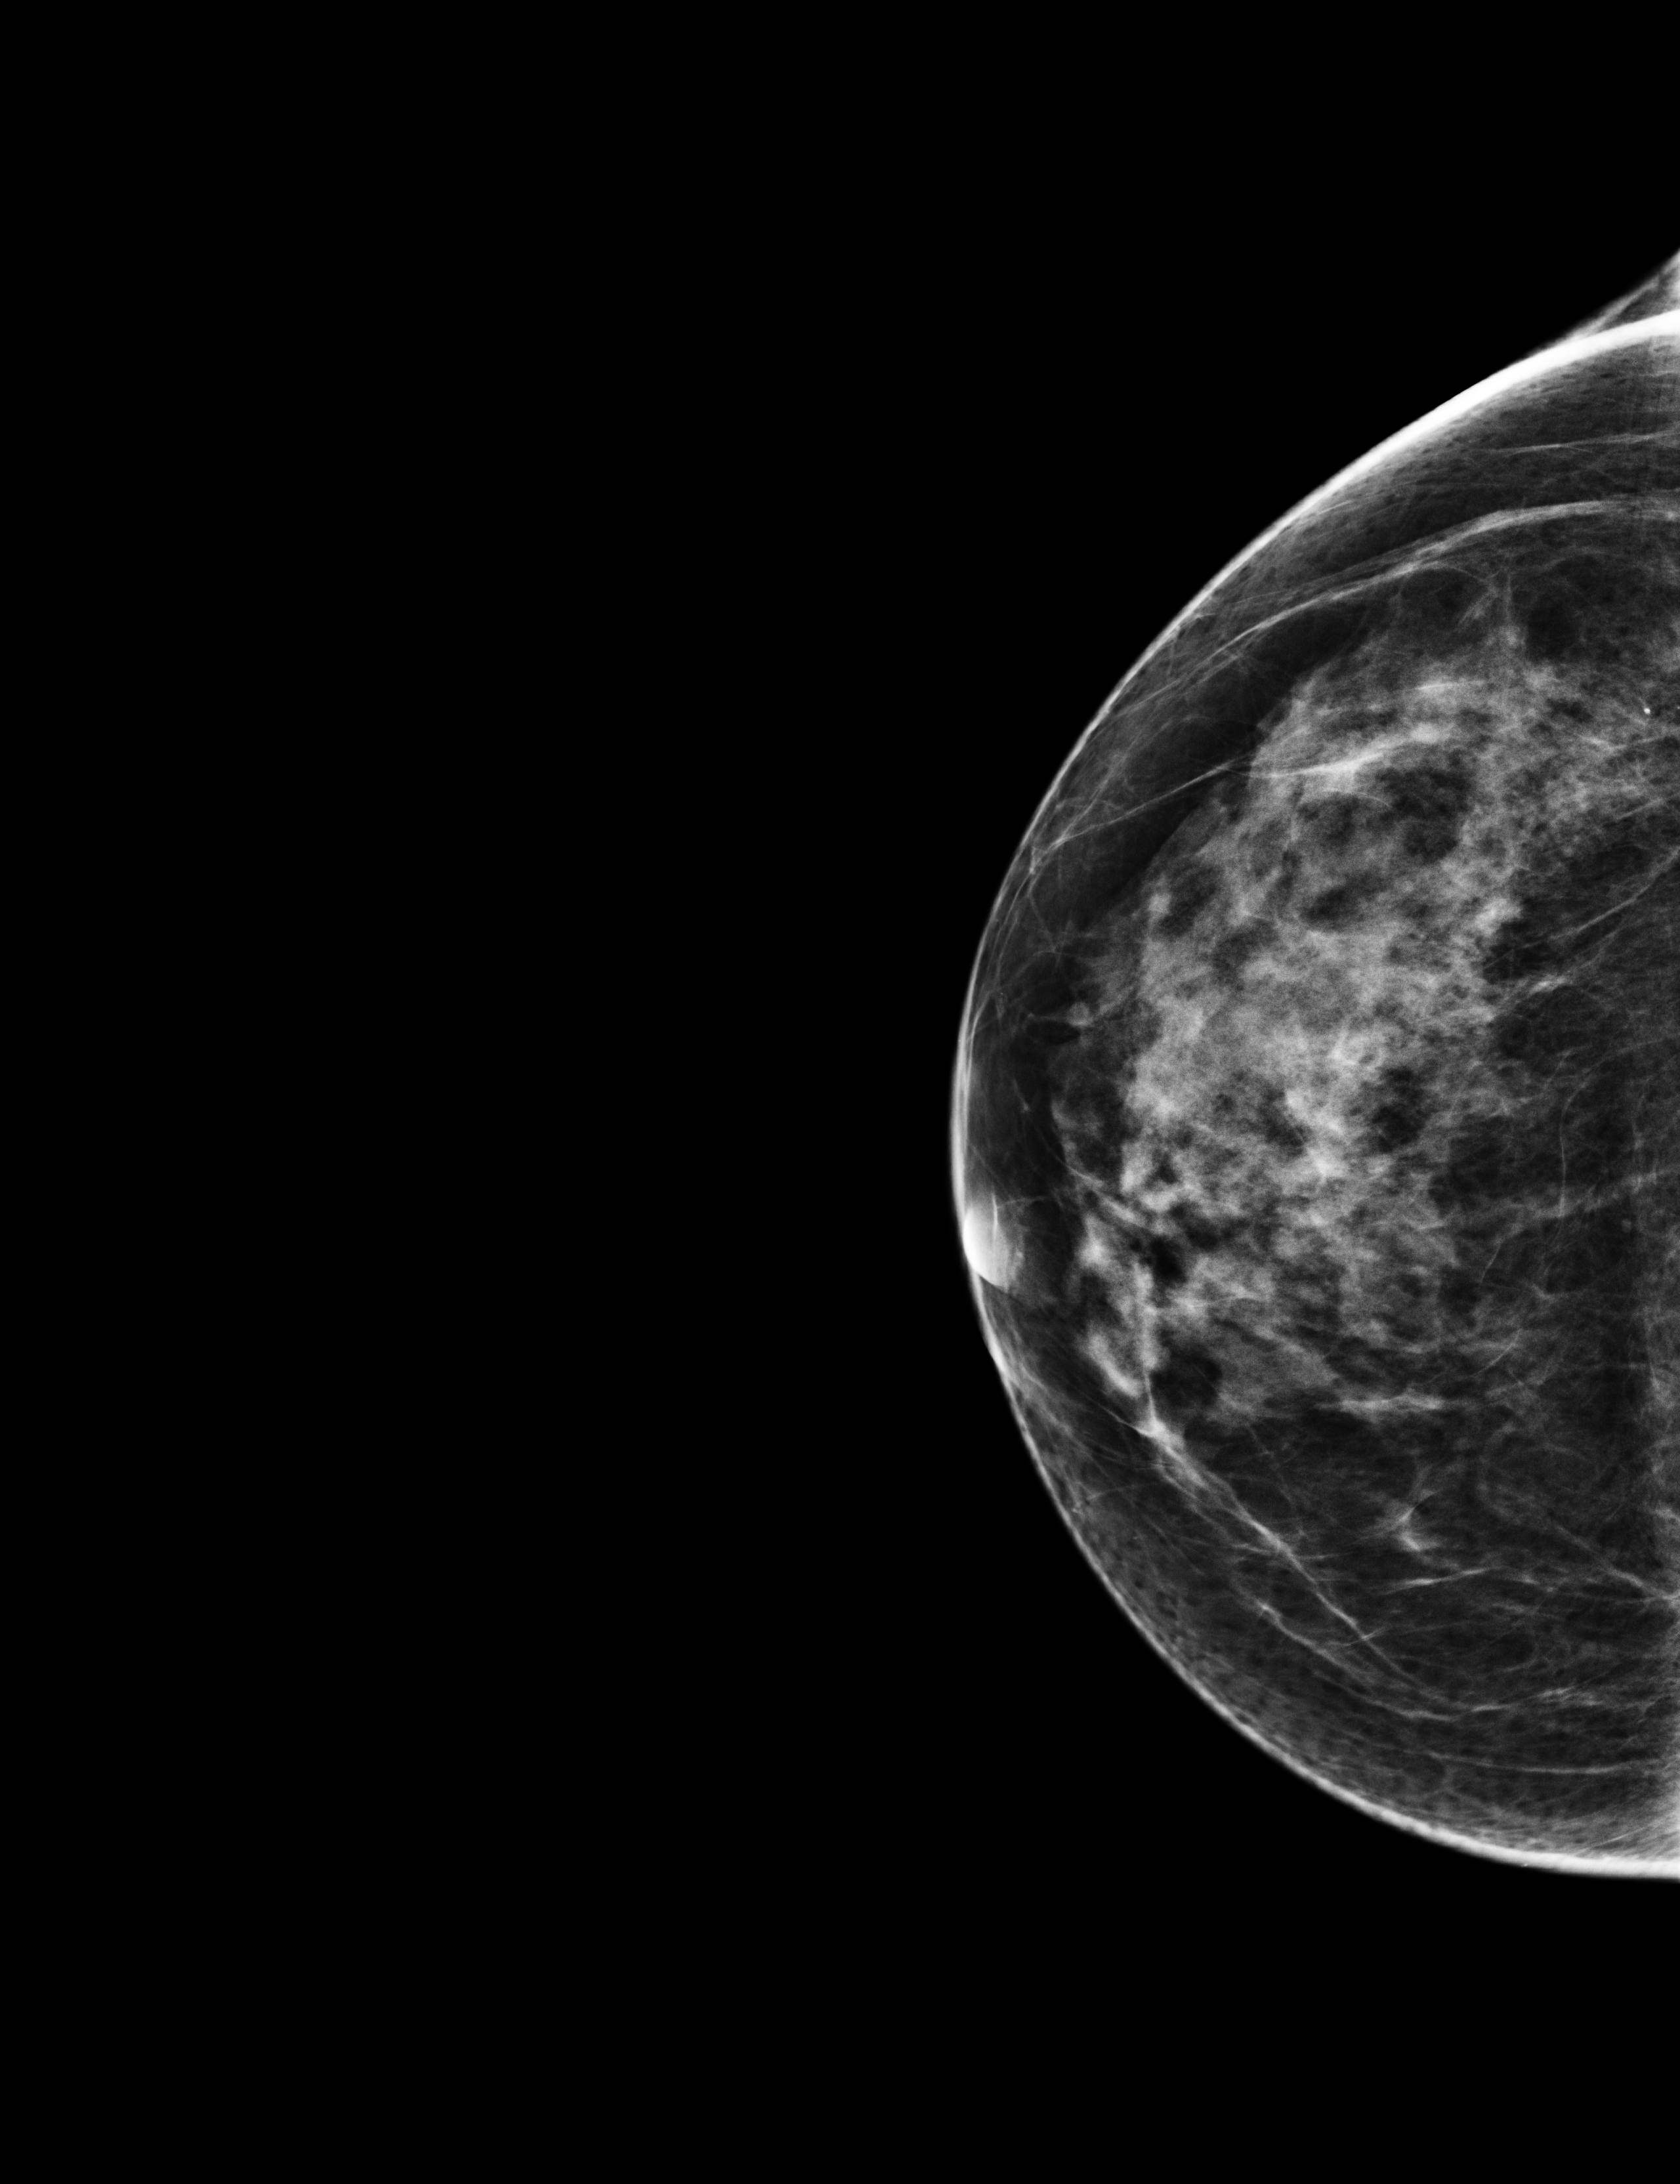
Screening examination.
Image type: full-field digital mammogram. Breast: right. Projection: cranio-caudal projection.